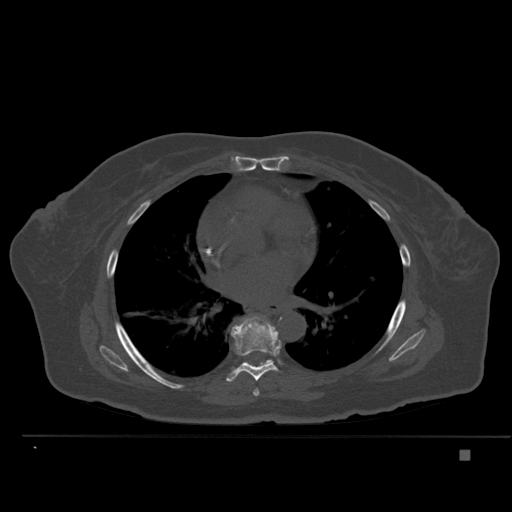
CT including the spine, one axial slice. Slice 324 of 477 in the series (ordered by position). Bone window (W 1800 / L 400 HU). 1.5 mm slice thickness. 512 × 512 image matrix. Female patient, age 74 years. Case-level facts recorded for this patient, not image findings: primary cancer: colon.
Annotated regions visible in this slice (semi-automatic segmentation, software-assisted and operator-edited):
- T6 vertebra: bounding box [x1, y1, x2, y2] px = [253, 389, 260, 396]
- T7 vertebra: [226, 318, 279, 382]
- T8 vertebra: [244, 316, 274, 364]